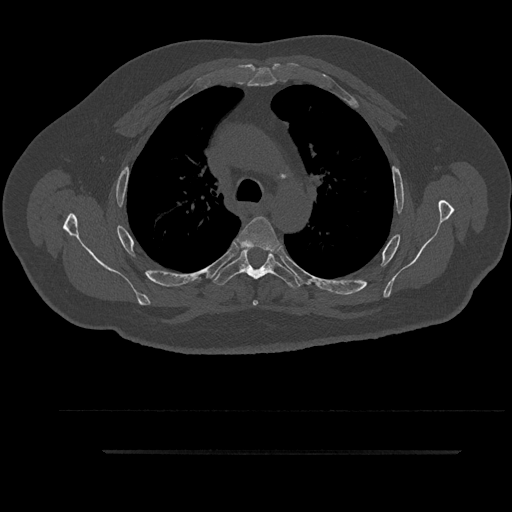
CT including the spine, one axial slice; position 647 of 797 along the scan axis; reconstruction kernel Br40s/3; 120 kVp; bone window (W 1800 / L 400 HU); 0.5 mm slice thickness; 512 × 512 image matrix, field of view 432 × 432 mm. Male patient, age 63 years. Case-level facts recorded for this patient, not image findings: primary cancer: renal.
Structures marked on this image (semi-automatic segmentation, software-assisted and operator-edited):
- T4 vertebra: bounding box <237,216,281,306> (left, top, right, bottom; pixels)
- T5 vertebra: <214,246,300,290>